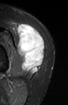
MRI of an extremity soft-tissue mass, one axial slice; slice 32 of 52 in the series (ordered by position); STIR; MR volume resampled by the dataset authors to the PET/CT grid (not the native acquisition matrix); 68 × 105 image matrix, field of view 66 × 103 mm. Female patient. Case-level facts recorded for this patient, not image findings: histological type: spindle cell suggestive of biphasic synovial sarcoma; grade: intermediate; site of the primary tumour: left knee.
Annotated regions visible in this slice (expert contour drawn on MRI and transferred to this co-registered scan by the dataset authors):
- gross tumour volume including surrounding oedema: bounding box (x1, y1, x2, y2) in pixels: (17, 24, 45, 73)
- gross tumour volume (mass): (17, 25, 45, 73)